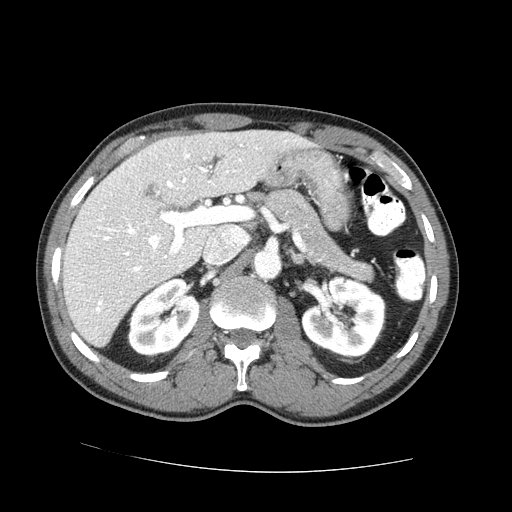
Contrast-enhanced abdominal CT (liver protocol), one axial slice. Slice 40 of 73 in the series (ordered by position). Reconstruction kernel STANDARD. 100 kVp. One of 2 acquisitions stored at this slice position. Soft-tissue window (W 400 / L 40 HU). 2.5 mm slice thickness. 512 × 512 image matrix. From the clinical record (not read from this slice): diagnosis: hepatocellular carcinoma (patient treated with transarterial chemoembolisation; whether this scan precedes or follows treatment is not stated here); TNM stage (as recorded): Stage-IVA; Child-Pugh class: A; tumour differentiation: no biopsy.
Structures marked on this image (semi-automatically segmented with operator editing):
- liver parenchyma outside the tumour (the mass and vessels are separate outlines, so this box may not span the whole liver): bounding box [x1, y1, x2, y2] px = [62, 130, 309, 346]
- mass: [144, 183, 154, 196]
- liver vessels: [93, 144, 243, 313]